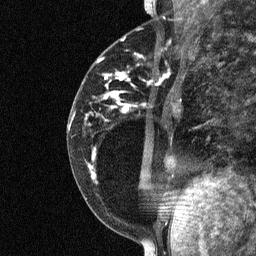
Breast MRI (dynamic contrast-enhanced), one sagittal slice. Slice 25 of 64 in the series (ordered by position). Dynamic contrast-enhanced study with each time point stored as its own series, time point 2 of 3 at this slice position (early post-contrast, ordered by acquisition time). 1.5 T. TE 4.8 ms, TR 27 ms. 256 × 256 image matrix, field of view 180 × 180 mm. Patient: female, 34 years. From the clinical record (not read from this slice): setting: breast cancer imaged before/during neoadjuvant chemotherapy; receptor status: HR-positive, HER2-negative.
Structures marked on this image (semi-automatically segmented with operator editing):
- analysis volume of interest (the breast-tissue region the enhancement analysis was run in; not a lesion): bounding box [x1, y1, x2, y2] px = [78, 44, 181, 191]
- tumour enhancement mask (voxels above the 90 % enhancement threshold inside the analysis volume of interest): [94, 74, 123, 175]